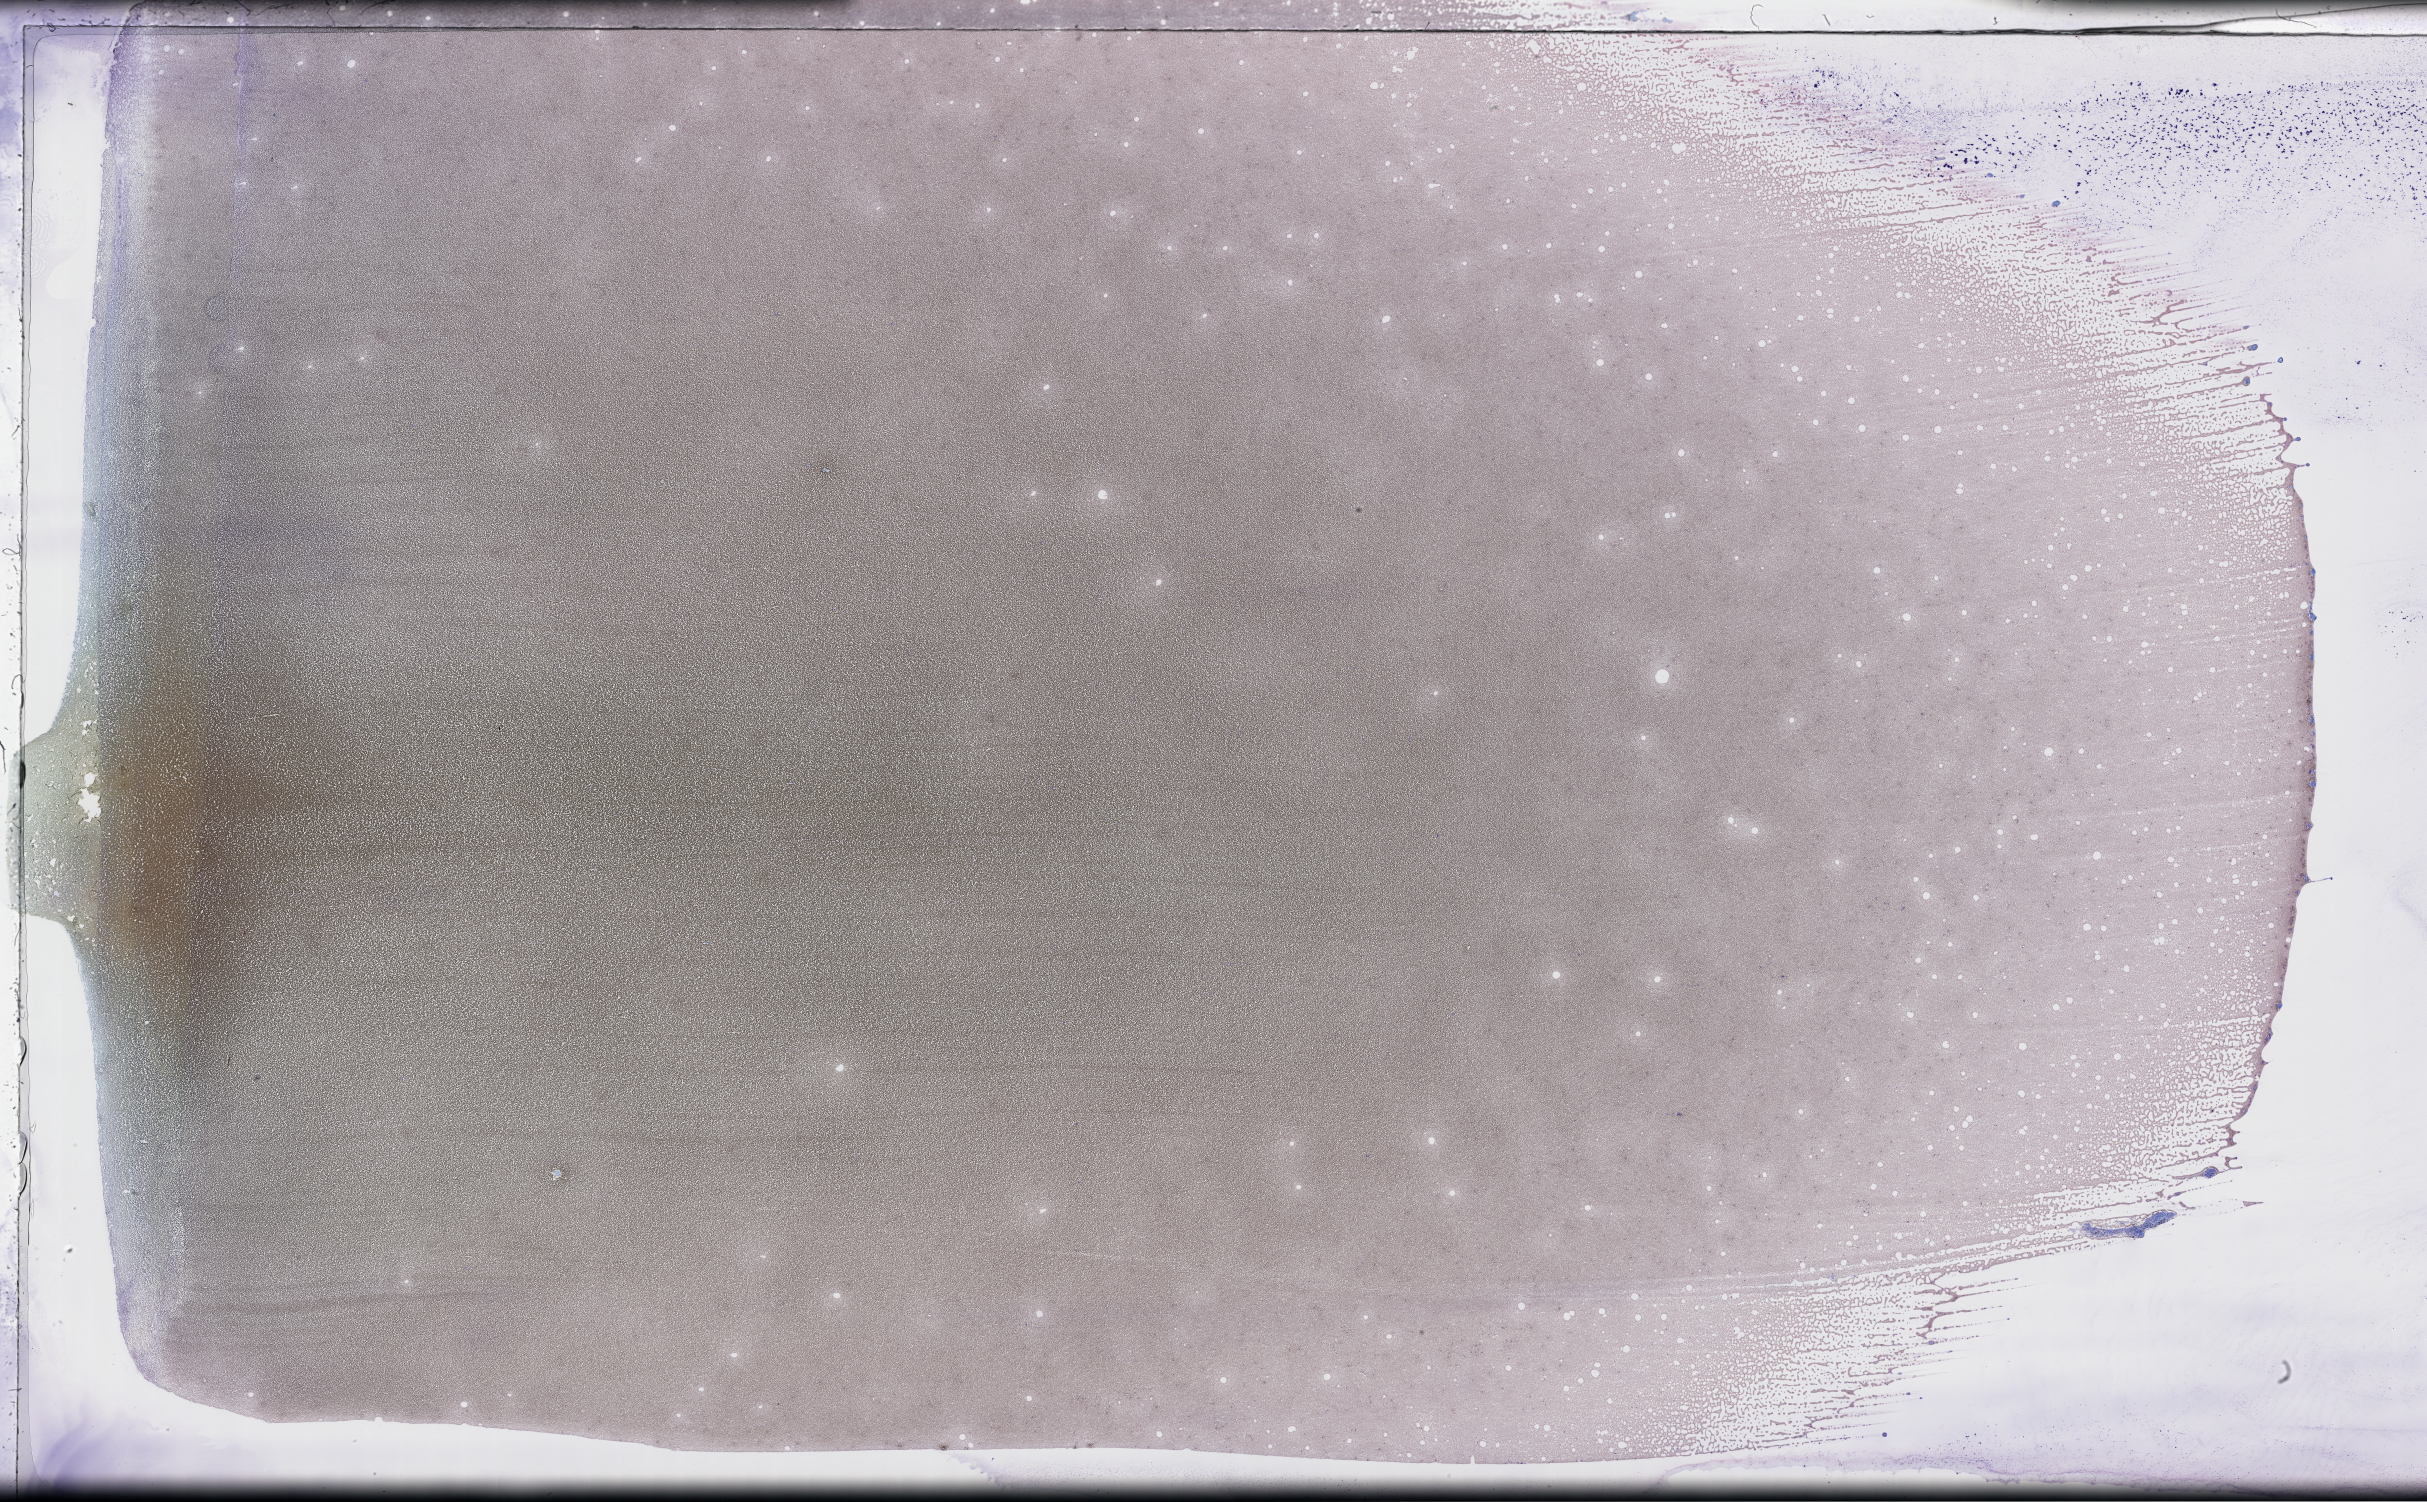
Wright–Giemsa-stained whole blood smear, whole-slide image, low-resolution overview of the scanned area, about 39.2 x 24.3 mm, specimen time point: collected on treatment. Patient: female.
* patient diagnosis: Plasma Cell Myeloma